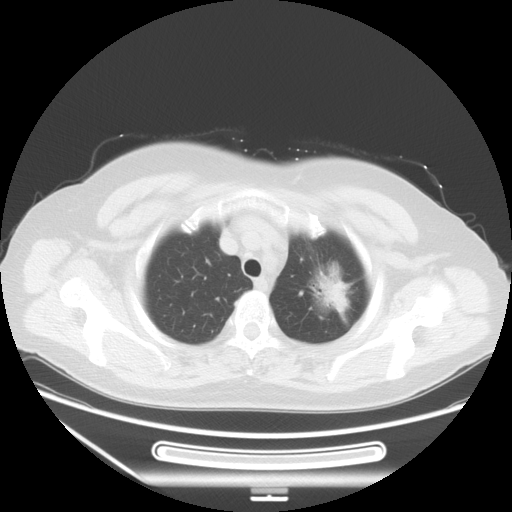
Chest CT, one axial slice; slice 46 of 53 in the series (ordered by position); lung window (W 1500 / L -600 HU); 512 × 512 image matrix, field of view 403 × 403 mm. Patient: female, 66 years. From the clinical record (not read from this slice): clinical TNM (as recorded): T2 N0 M0; histopathological grade: G2.
Structures marked on this image (bounding box drawn by a radiologist):
- lung tumour (recorded histology: adenocarcinoma): bounding box [x1, y1, x2, y2] px = [298, 243, 361, 341]